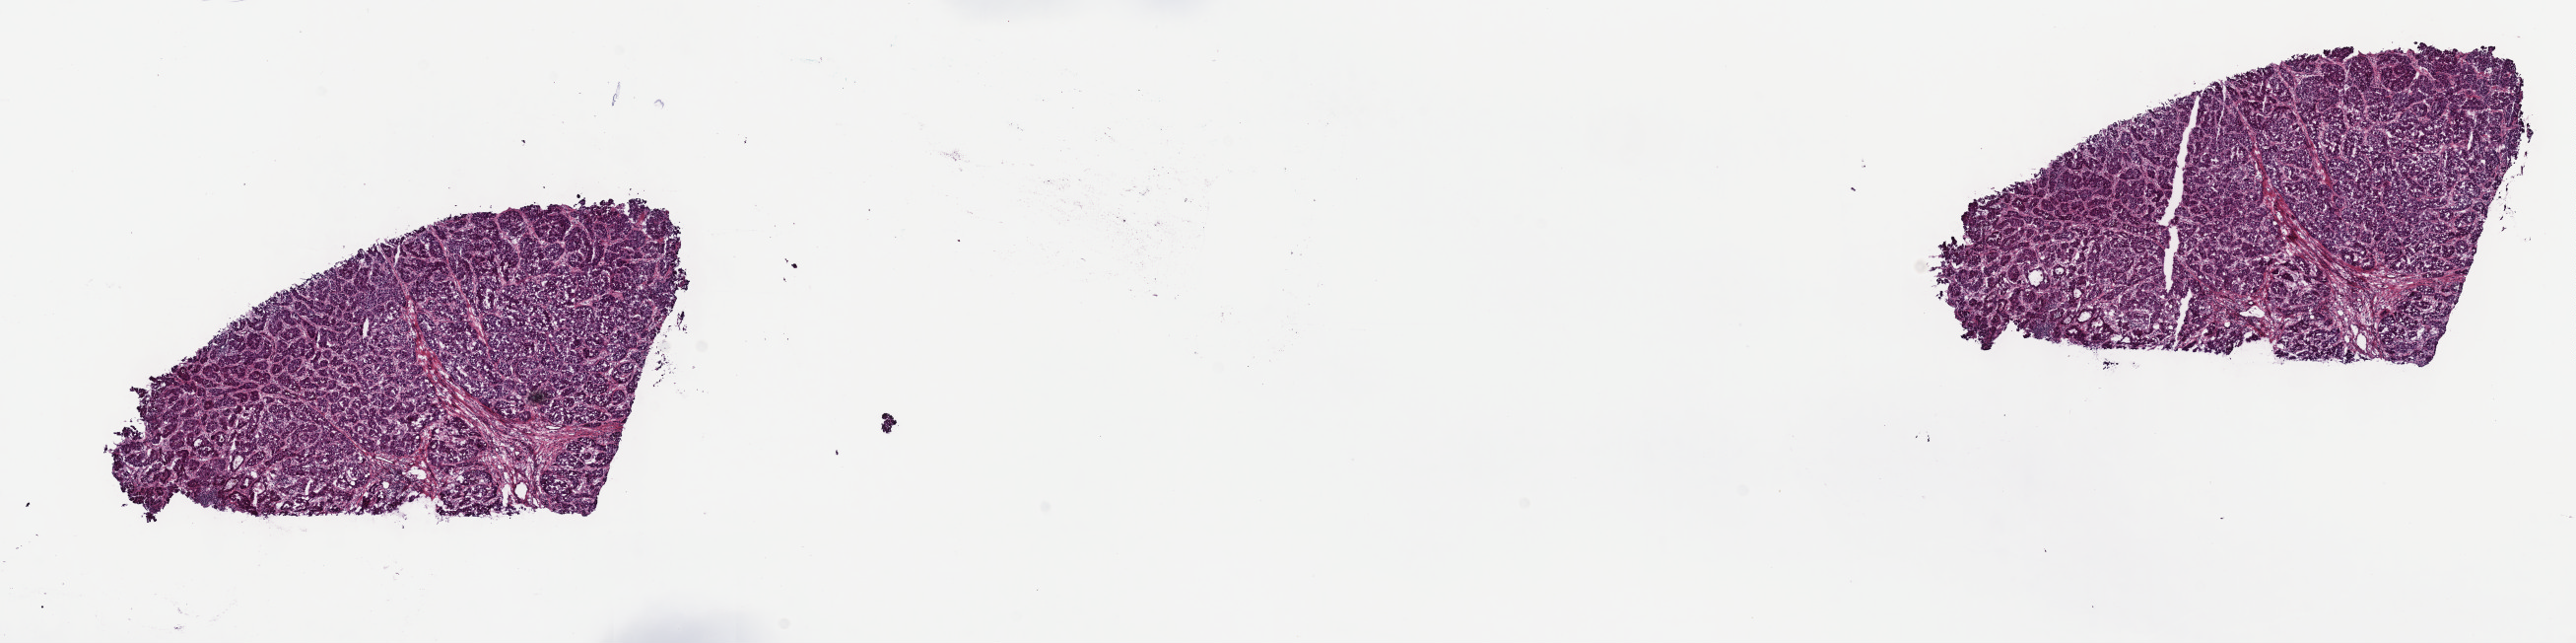
Whole-slide histology image, H&E-stained — shown as a low-resolution overview of the whole scanned area (about 21.1 x 5.3 mm, acquisition: 40x scan); frozen section from the top of the tissue portion; primary tumour sample from the liver. Male, age 59 years at initial diagnosis. Histologic grade: G3 (poorly differentiated). Slide review estimates, as recorded: tumour cells 100%, tumour nuclei 90%, normal cells 0%, stromal cells 0%, necrosis 0%. Infiltration values recorded for this section: lymphocyte infiltration 0%, monocyte infiltration 0%, neutrophil infiltration 0%.
* AJCC pathologic stage: I (7th edition)
* pathologic diagnosis: Hepatocellular carcinoma, NOS